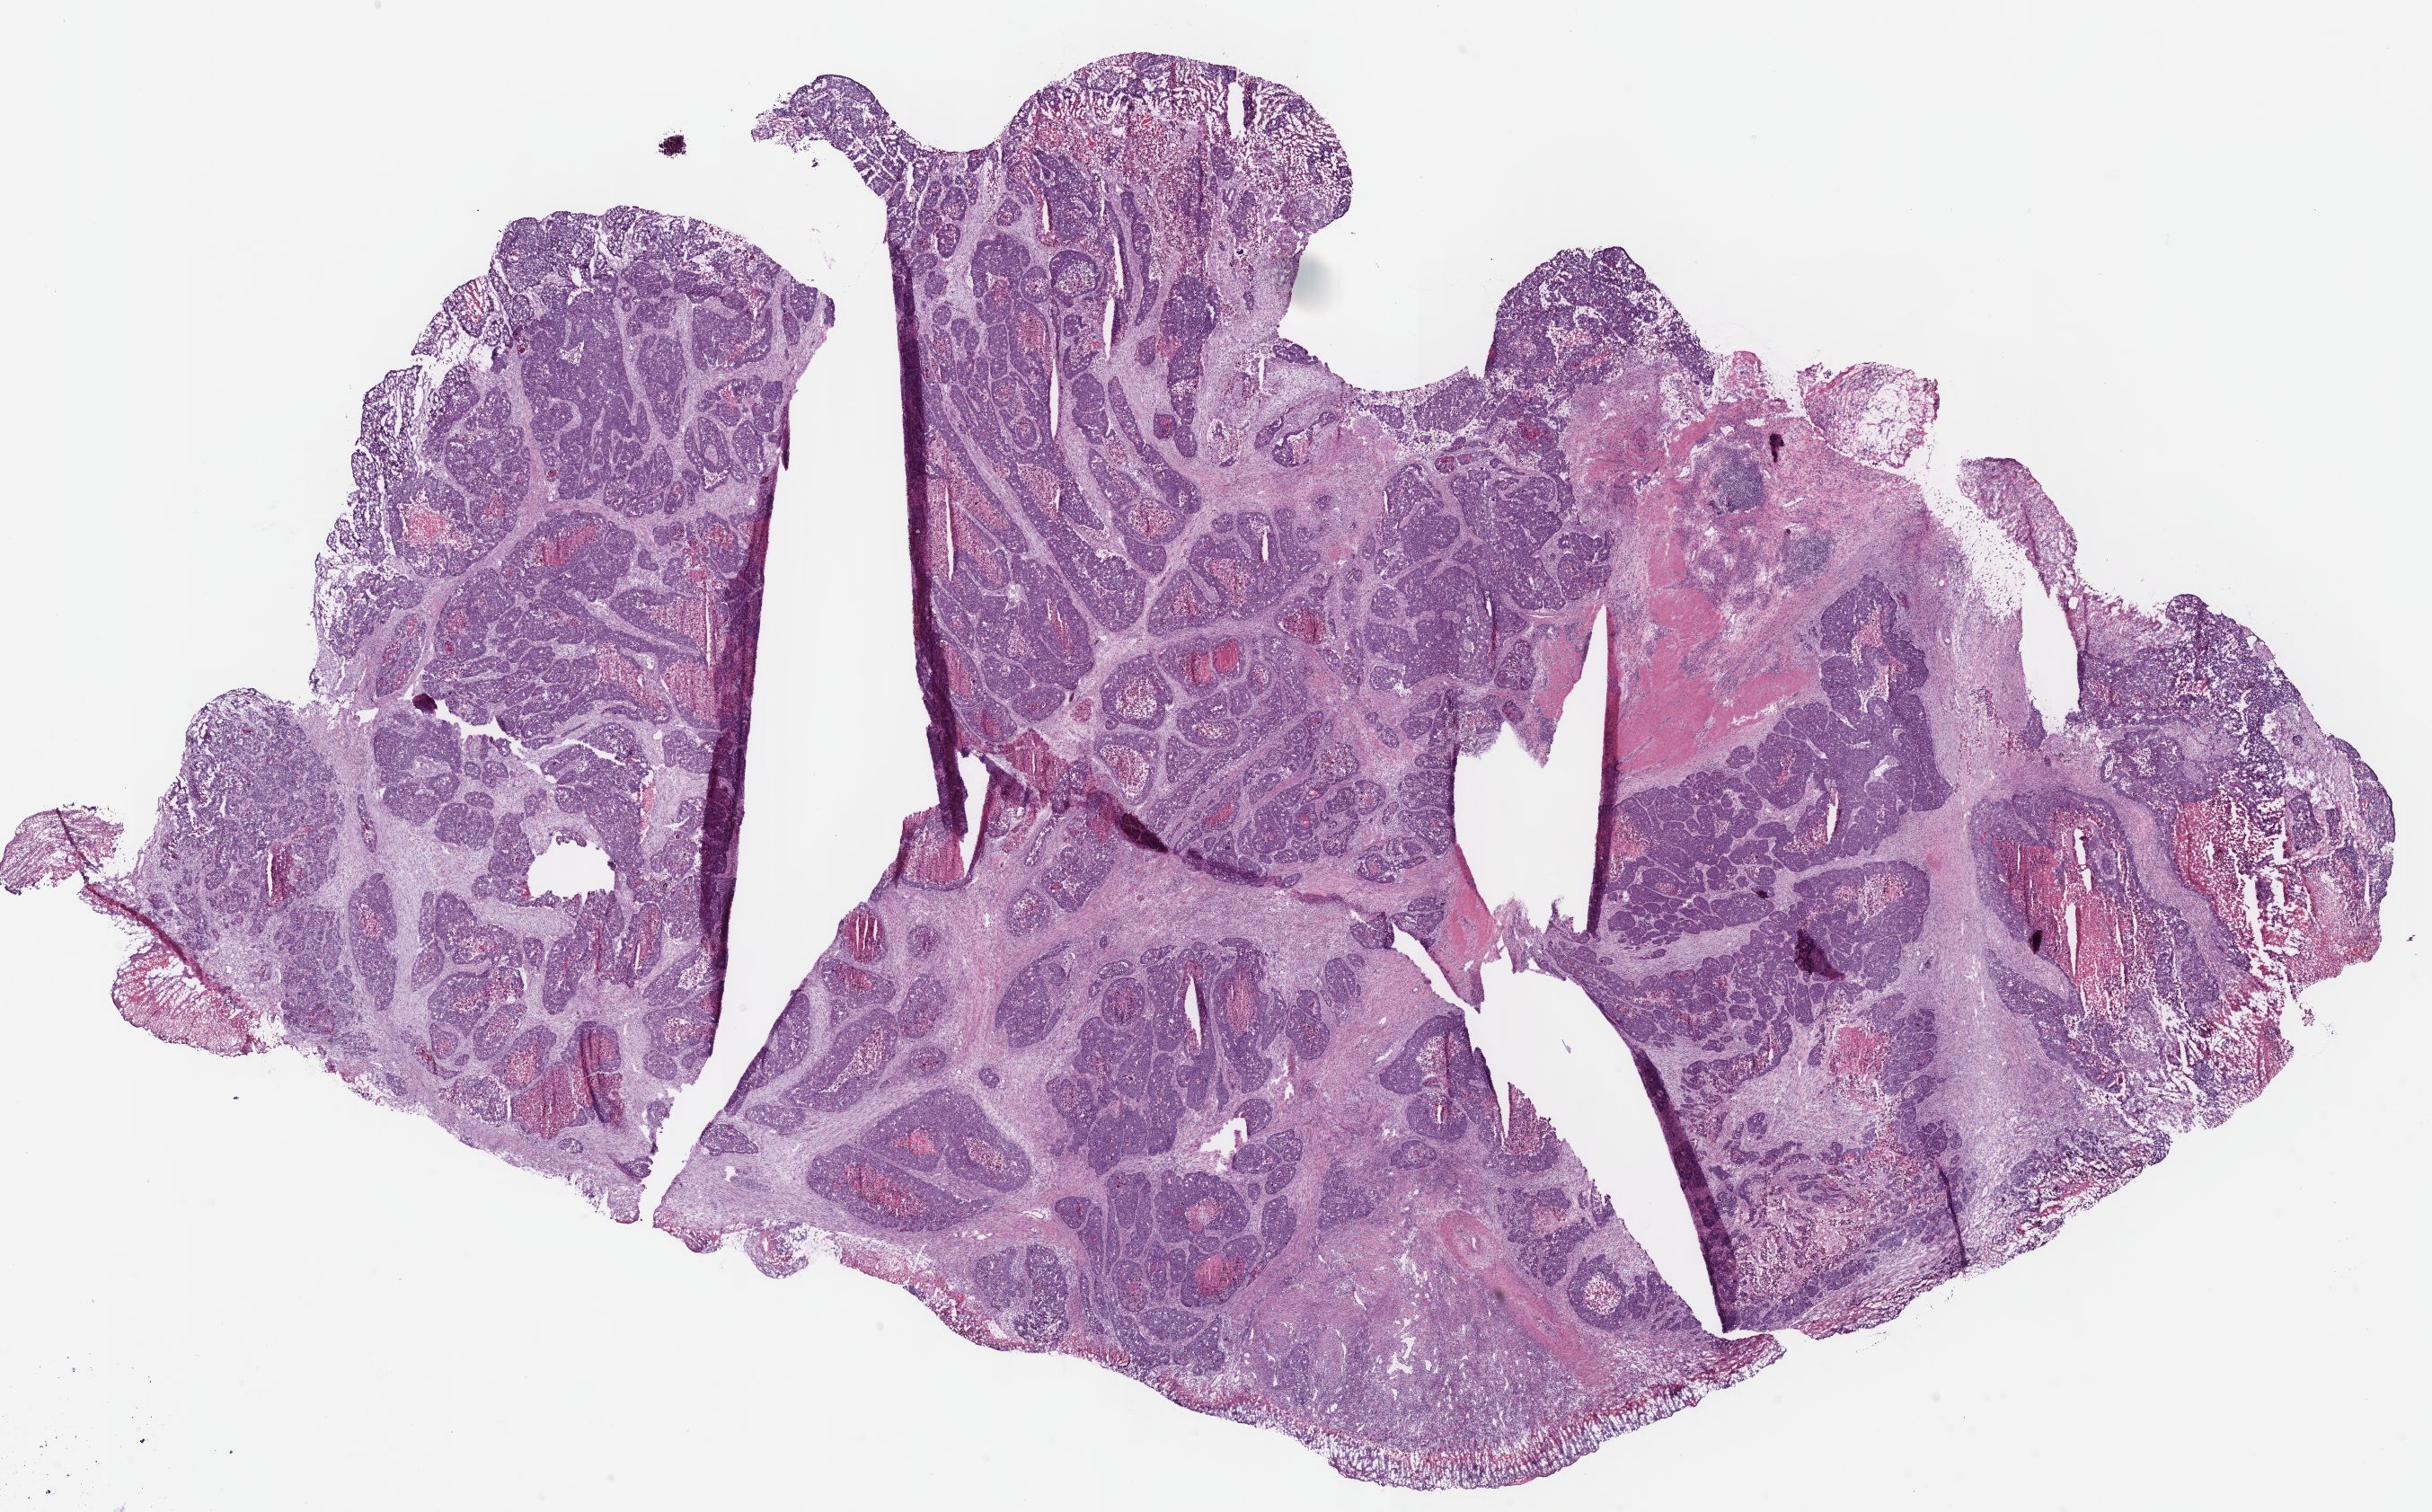
Digitized H&E-stained tissue section (whole slide), a low-resolution overview of the entire scanned area, about 21.3 x 13.3 mm (acquisition: 40x scan), frozen section from the bottom of the tissue portion, stomach, primary tumour sample. Patient: male, age at initial diagnosis 76 years. Histologic grade: G2 (moderately differentiated). Pathologist review of this section (percent, as recorded): tumour cells 84%, tumour nuclei 85%, normal cells 0%, stromal cells 4%, necrosis 12%. Inflammatory infiltration, as recorded: lymphocyte infiltration 10%, monocyte infiltration 0%, neutrophil infiltration 0%.
AJCC pathologic stage: IB (7th edition). Diagnosis: Adenocarcinoma, NOS (fundus of stomach).